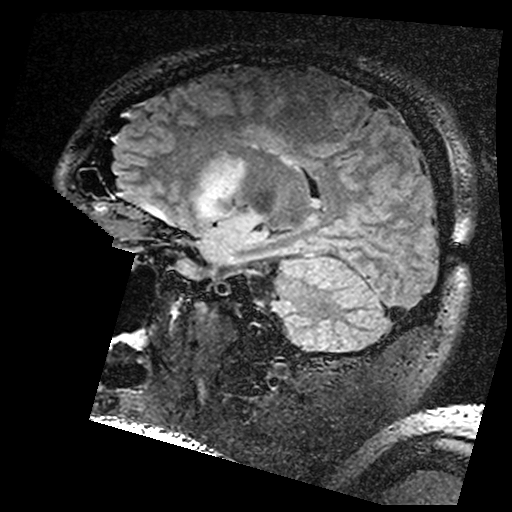
Brain MRI from a brain-tumour surgery series, one sagittal slice. Position 109 of 176 along the scan axis. T2 FLAIR. 512 × 512 image matrix. Case-level facts recorded for this patient, not image findings: histopathology: Astrocytoma; WHO grade: 3; IDH mutation: yes; tumour location: Left Insular.
Outlined on this slice (expert manual segmentation):
- residual tumour: bounding box [x1, y1, x2, y2] px = [204, 155, 247, 200]